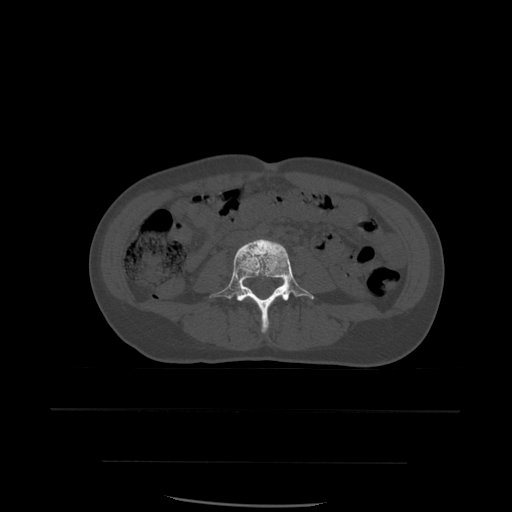
CT including the spine, one axial slice; bone window (W 1800 / L 400 HU); 1.25 mm slice thickness; 512 × 512 image matrix, field of view 392 × 392 mm. Patient age 48 years. From the clinical record (not read from this slice): primary cancer: lung; vertebrae with lytic lesions (as recorded): T11.
Outlined on this slice (semi-automatic segmentation, software-assisted and operator-edited):
- L4 vertebra: bounding box <210,239,314,333> (left, top, right, bottom; pixels)